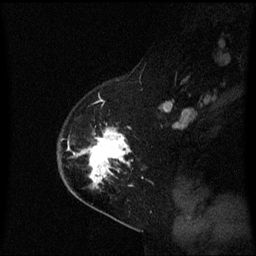
Breast MRI (dynamic contrast-enhanced), one sagittal slice; position 42 of 60 along the scan axis; dynamic contrast-enhanced series, image 2 of 3 at this slice position (ordered by acquisition); 1.5 T; TE 4.2 ms, TR 8.4 ms; 2 mm slice thickness; 256 × 256 image matrix. Patient: female, 54 years. From the clinical record (not read from this slice): setting: breast cancer imaged before/during neoadjuvant chemotherapy; receptor status: HER2-positive.
Annotated regions visible in this slice (semi-automatic segmentation, software-assisted and operator-edited):
- analysis volume of interest (the breast-tissue region the enhancement analysis was run in; not a lesion): bounding box [x1, y1, x2, y2] px = [60, 129, 134, 199]
- tumour enhancement mask (voxels above the 70 % enhancement threshold inside the analysis volume of interest): [79, 131, 132, 186]